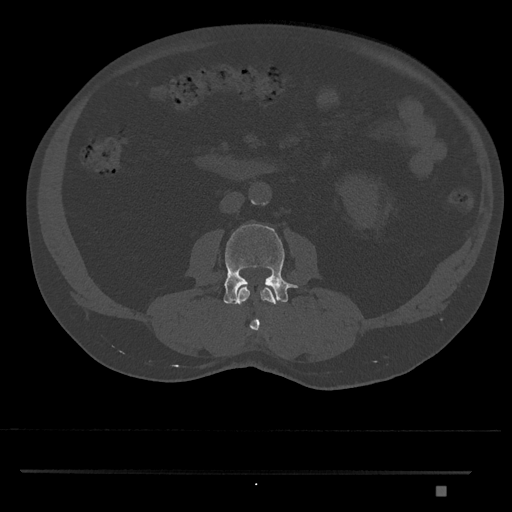
CT including the spine, one axial slice; slice 703 of 1134 in the series (ordered by position); 120 kVp; bone window (W 1800 / L 400 HU); 0.5 mm slice thickness; 512 × 512 image matrix. Patient: male, 65 years. Case-level facts recorded for this patient, not image findings: primary cancer: prostate.
Structures marked on this image (semi-automatic segmentation, software-assisted and operator-edited):
- L2 vertebra: box from (x=237, y=287) to (x=276, y=331) px
- L3 vertebra: (x=223, y=224)–(x=298, y=305)